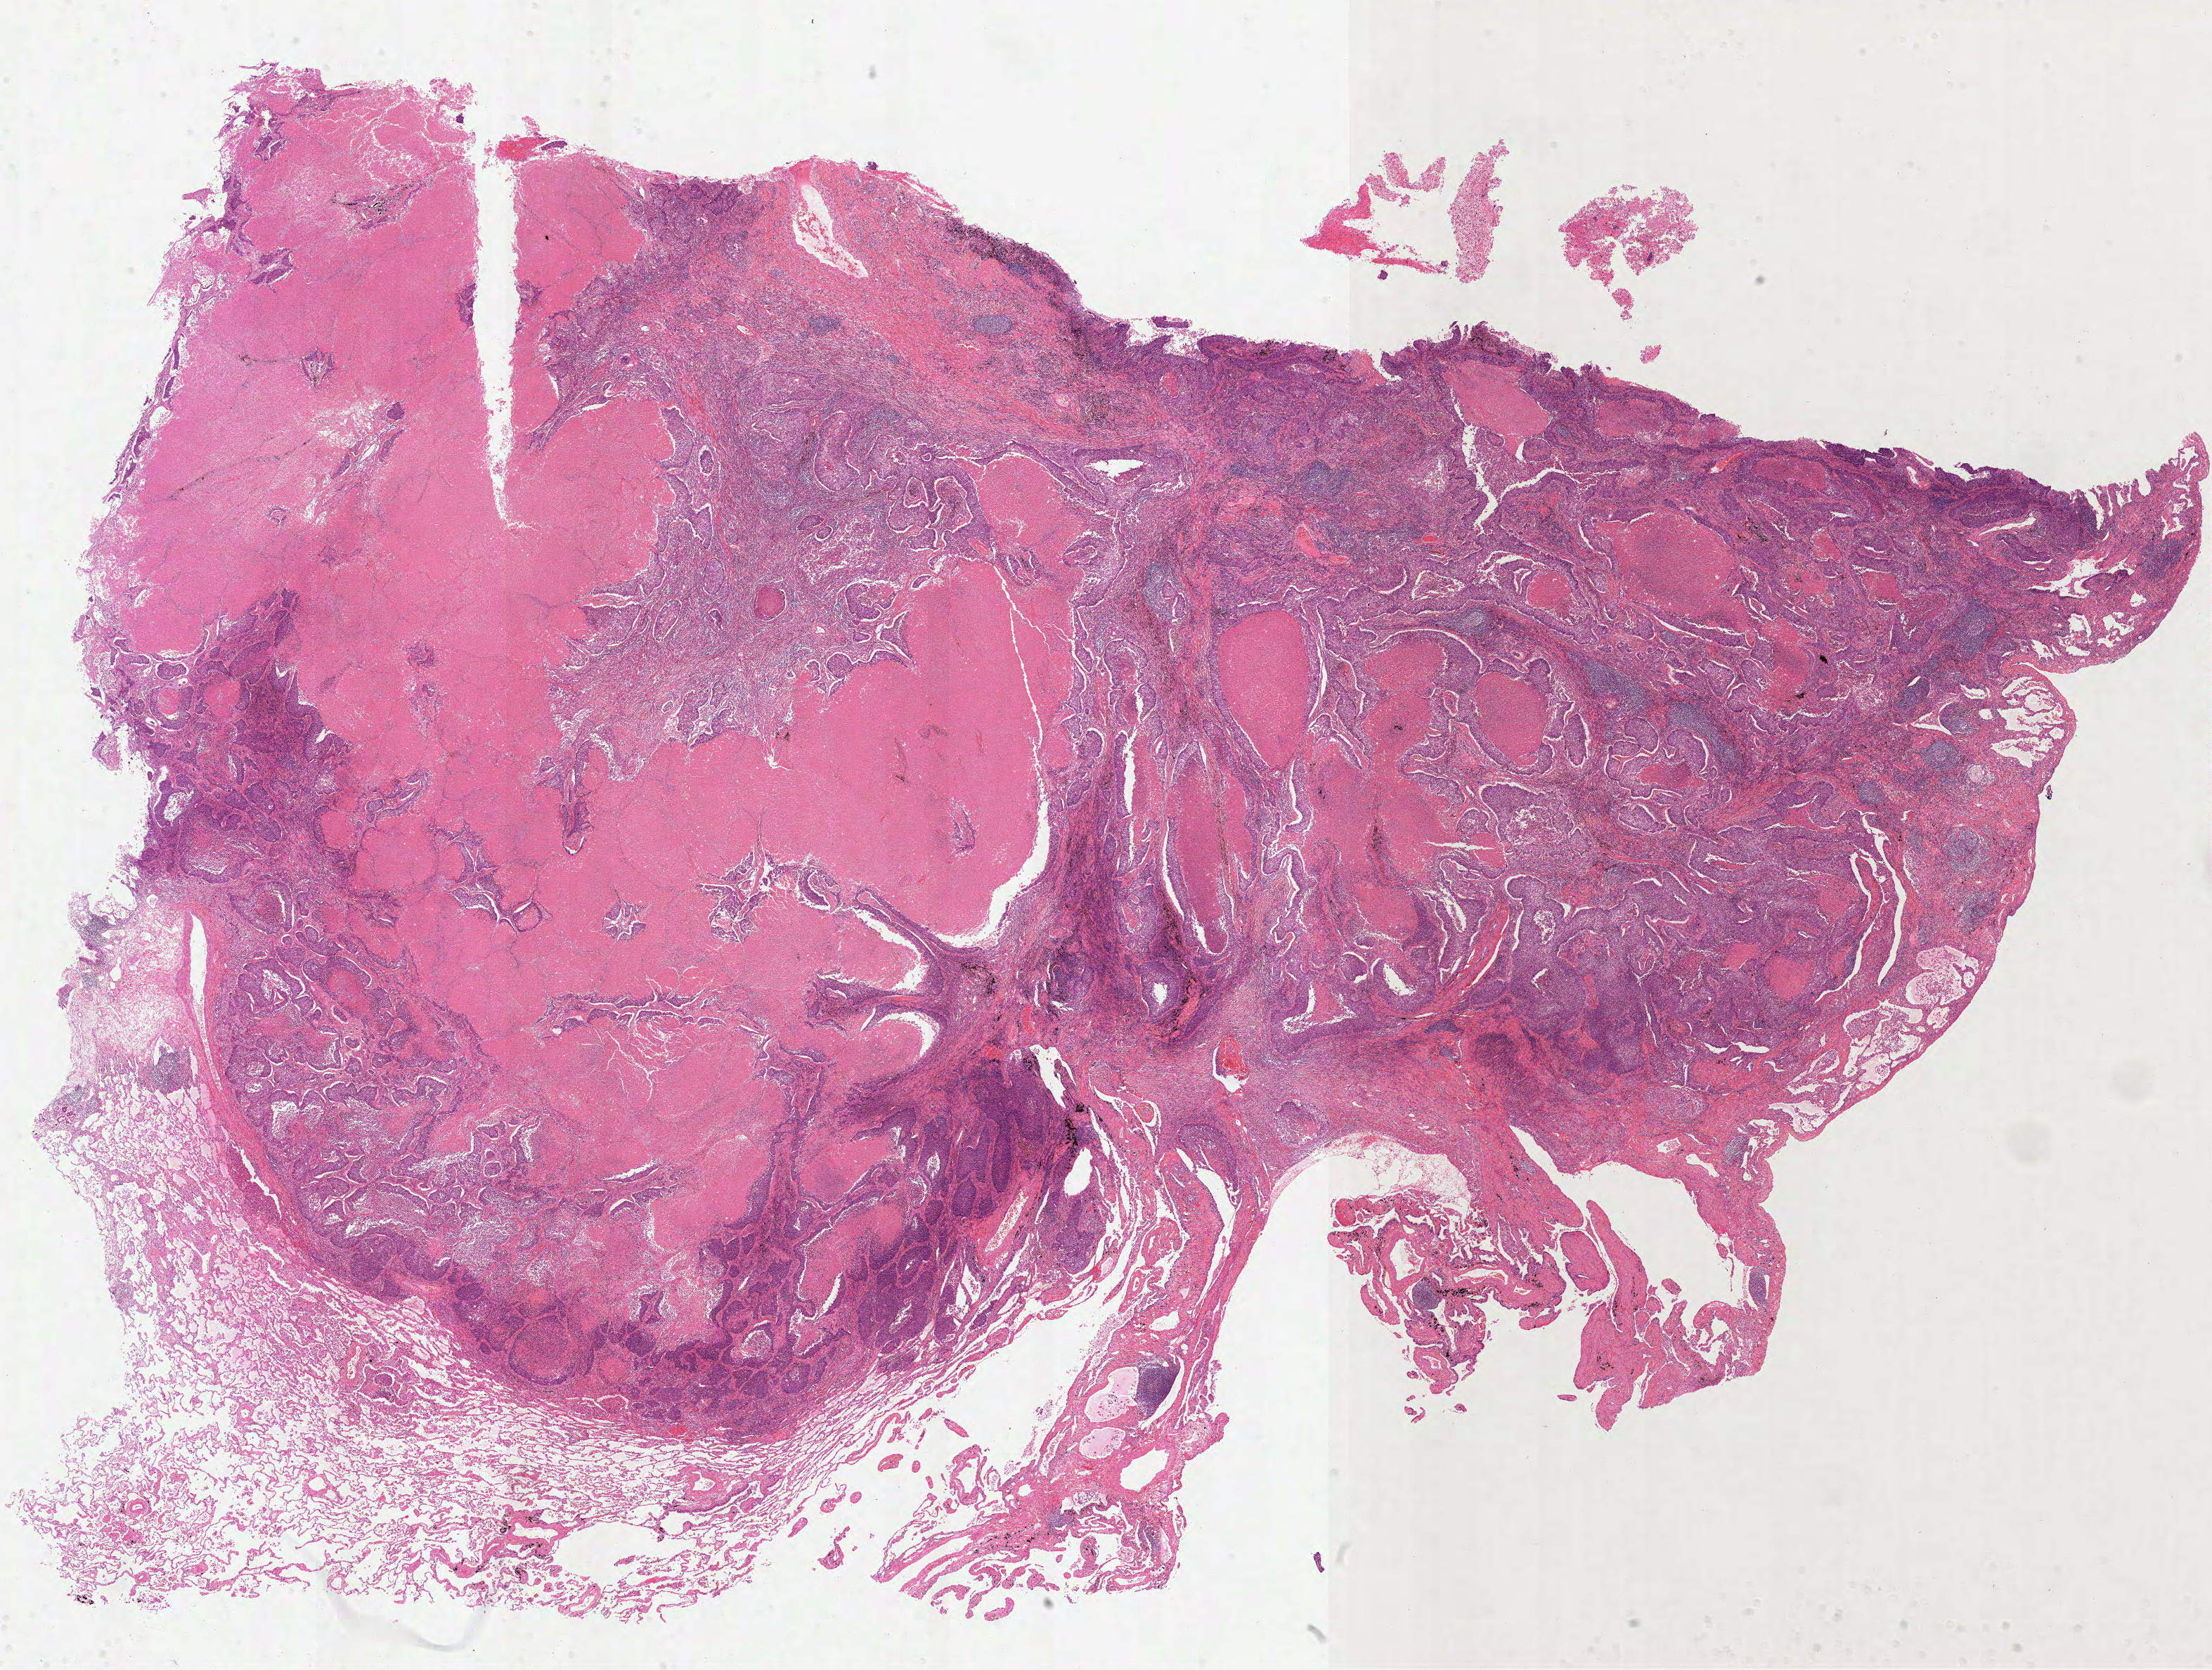
H&E-stained whole-slide image — shown as a low-resolution overview of the whole scanned area (about 25.4 x 19.2 mm); formalin-fixed paraffin-embedded (FFPE) diagnostic section; sample: primary tumour, lung. Male, age 60 years at initial diagnosis.
TNM: T2a N0 M0. AJCC pathologic stage: IB (7th edition). Histologic diagnosis: Squamous cell carcinoma, NOS (upper lobe, lung).